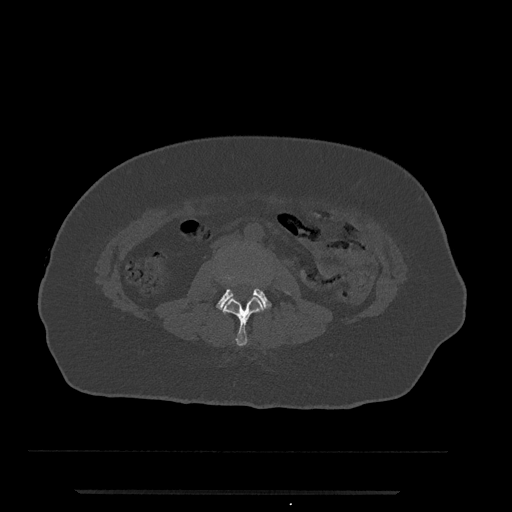
CT including the spine, one axial slice; position 2 of 797 along the scan axis; reconstruction kernel Br40s/3; 120 kVp; bone window (W 1800 / L 400 HU); 0.5 mm slice thickness; 512 × 512 image matrix, field of view 440 × 440 mm. Patient: female, 51 years. From the clinical record (not read from this slice): primary cancer: neuro; vertebrae with lytic lesions (as recorded): T8.
Annotated regions visible in this slice (semi-automatically segmented with operator editing):
- L2 vertebra: bounding box <222,294,265,346> (left, top, right, bottom; pixels)